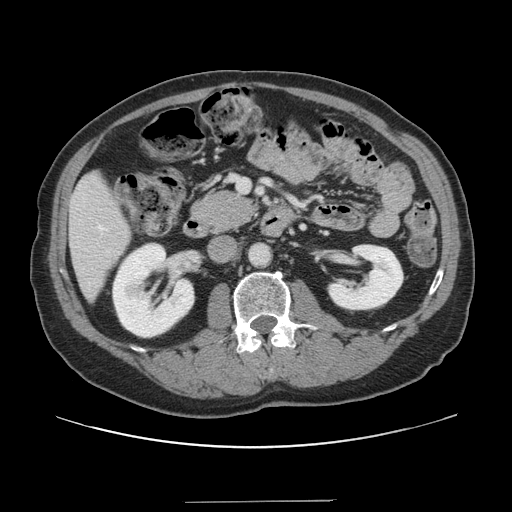
Contrast-enhanced abdominal CT, one axial slice. Slice 55 of 151 in the series (ordered by position). 120 kVp. Intravenous contrast given. Soft-tissue window (W 400 / L 40 HU). 2.5 mm slice thickness. 512 × 512 image matrix. Male patient, age 63 years. Case-level facts recorded for this patient, not image findings: diagnosis: colorectal cancer liver metastases, imaged before liver resection; multiple liver metastases: no; largest metastasis: 2.1 cm; disease in both lobes: no.
Outlined on this slice (outlined manually by an expert reader):
- hepatic veins: bounding box <99,226,103,230> (left, top, right, bottom; pixels)
- liver: <70,174,130,298>
- planned liver remnant (the part of the liver to remain after resection): <70,174,130,297>
- portal vein (with intrahepatic branches): <236,178,248,190>